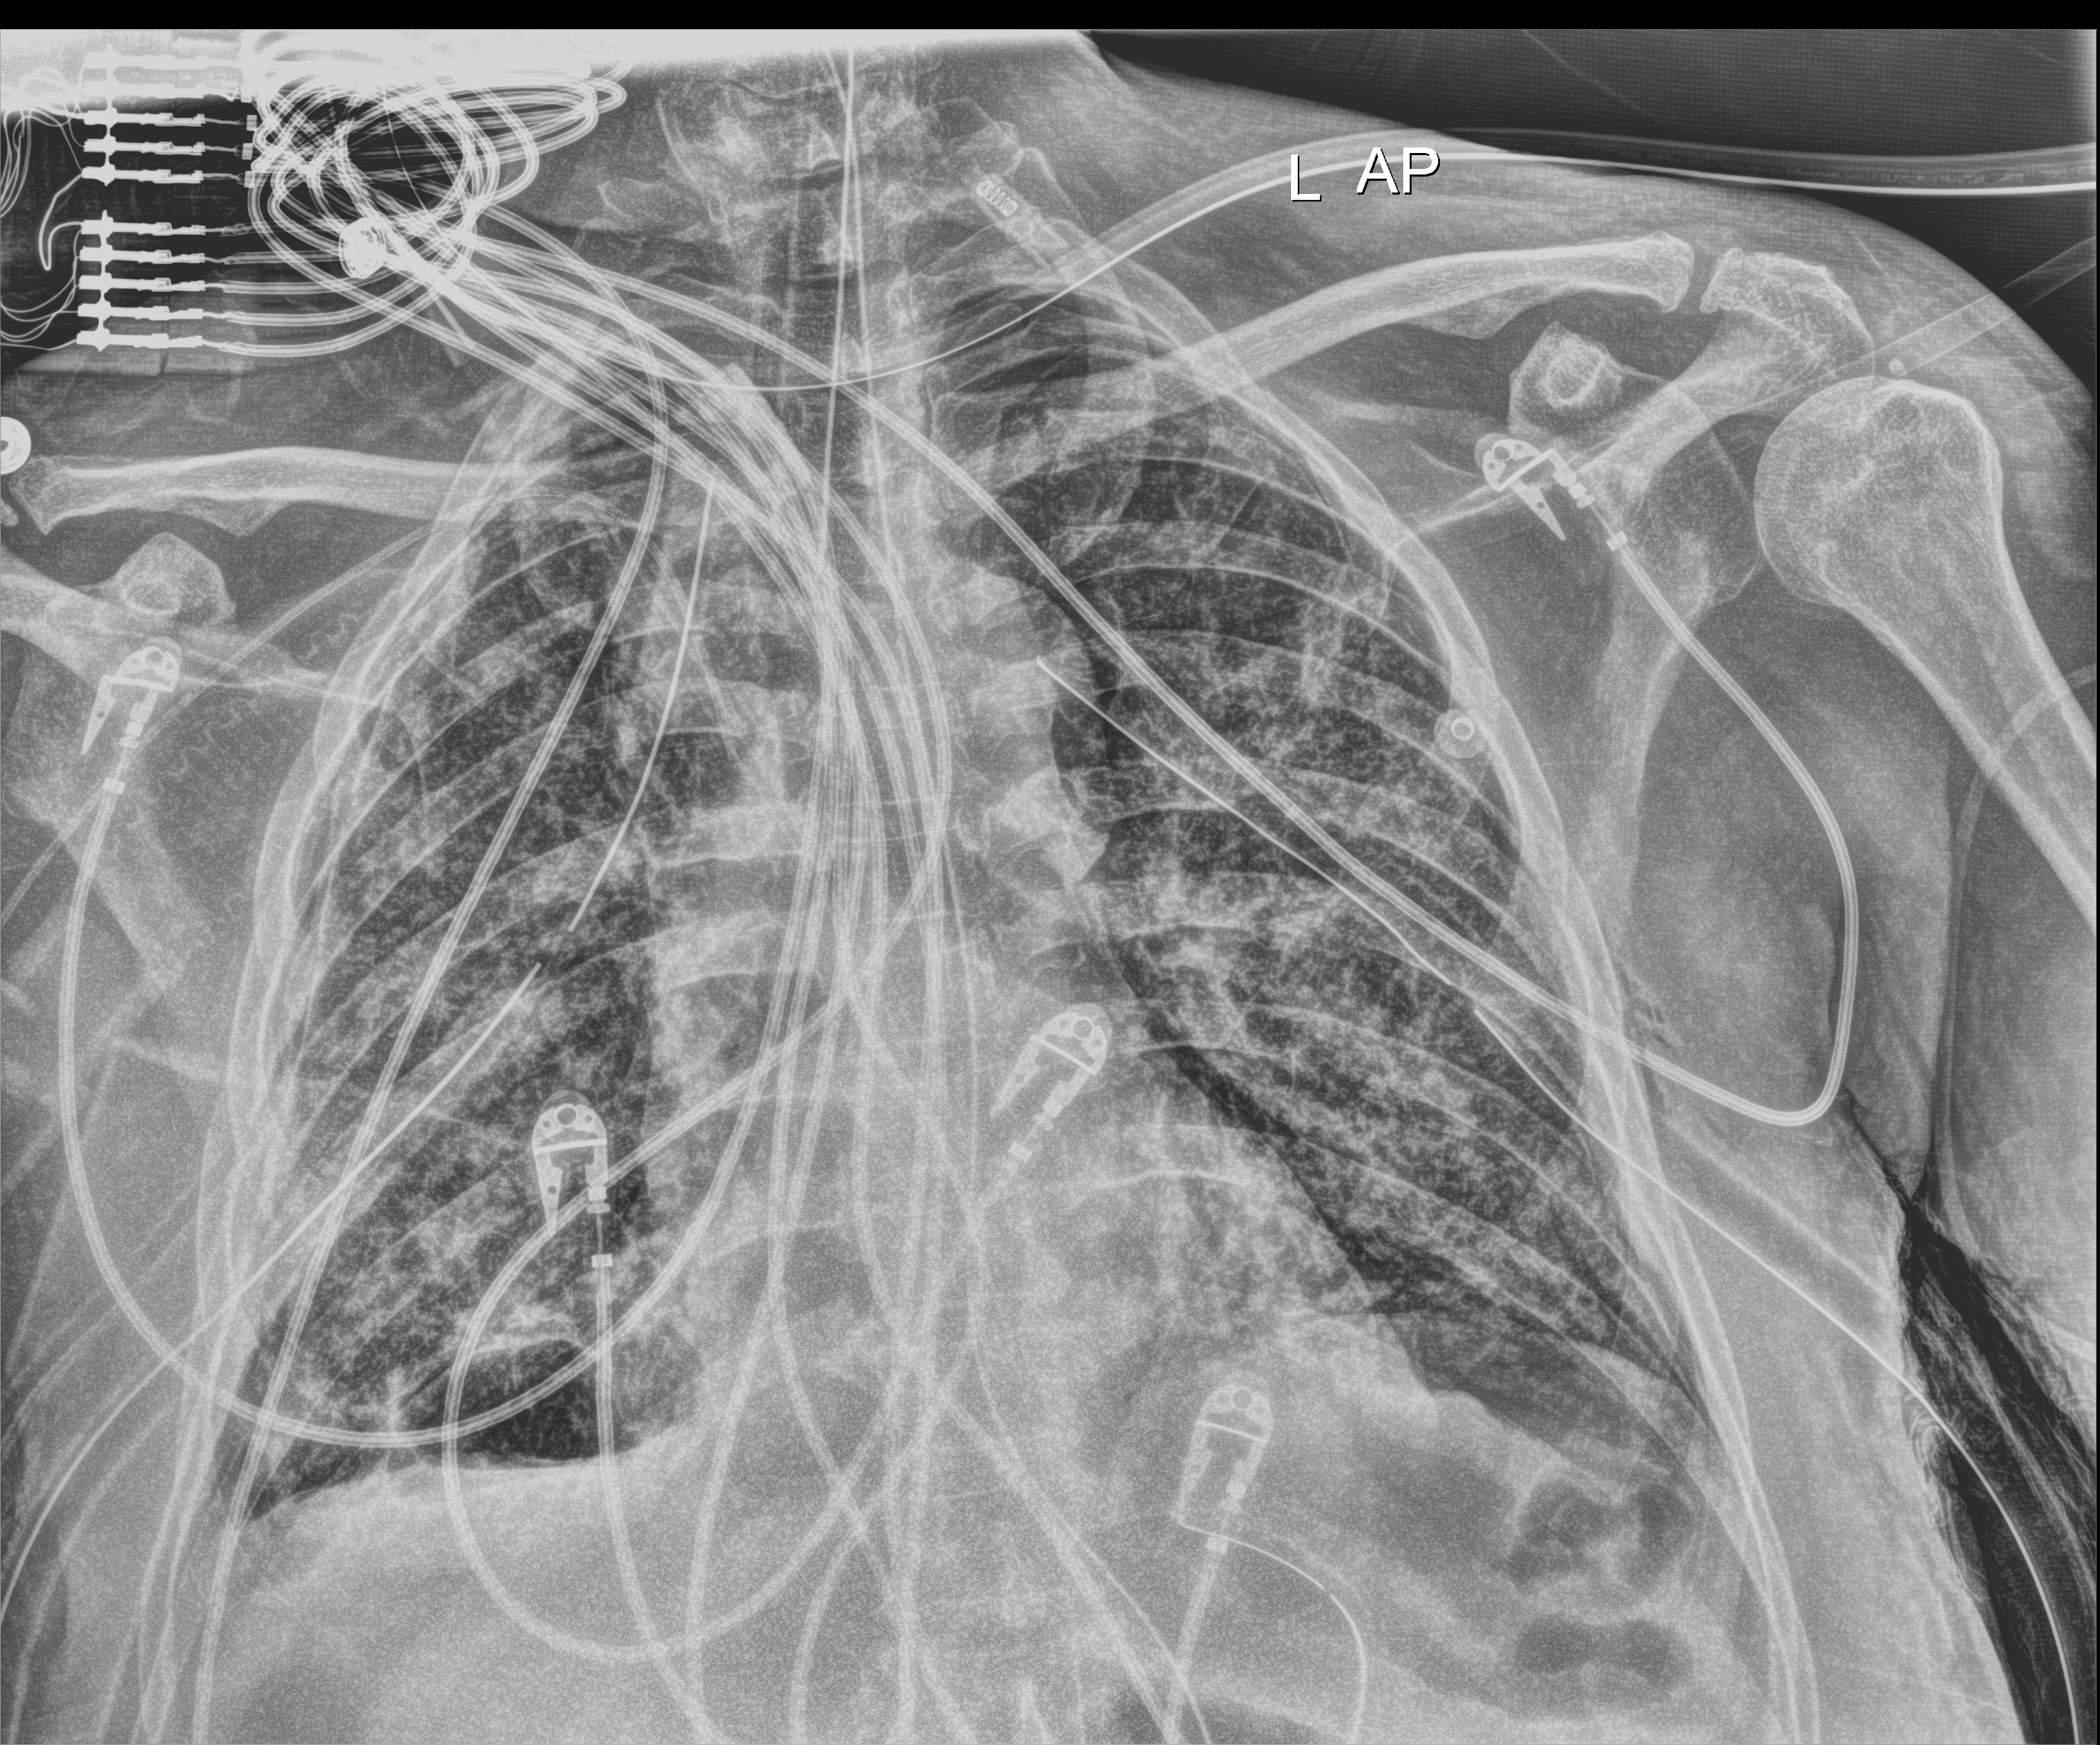
Portable chest radiograph; anteroposterior (AP) projection. Male patient hospitalised with COVID-19, age 60–74 years.
Hospital-stay facts (about this admission, not read from this image; timing relative to this image not recorded): other chronic lung disease (admission record): no.